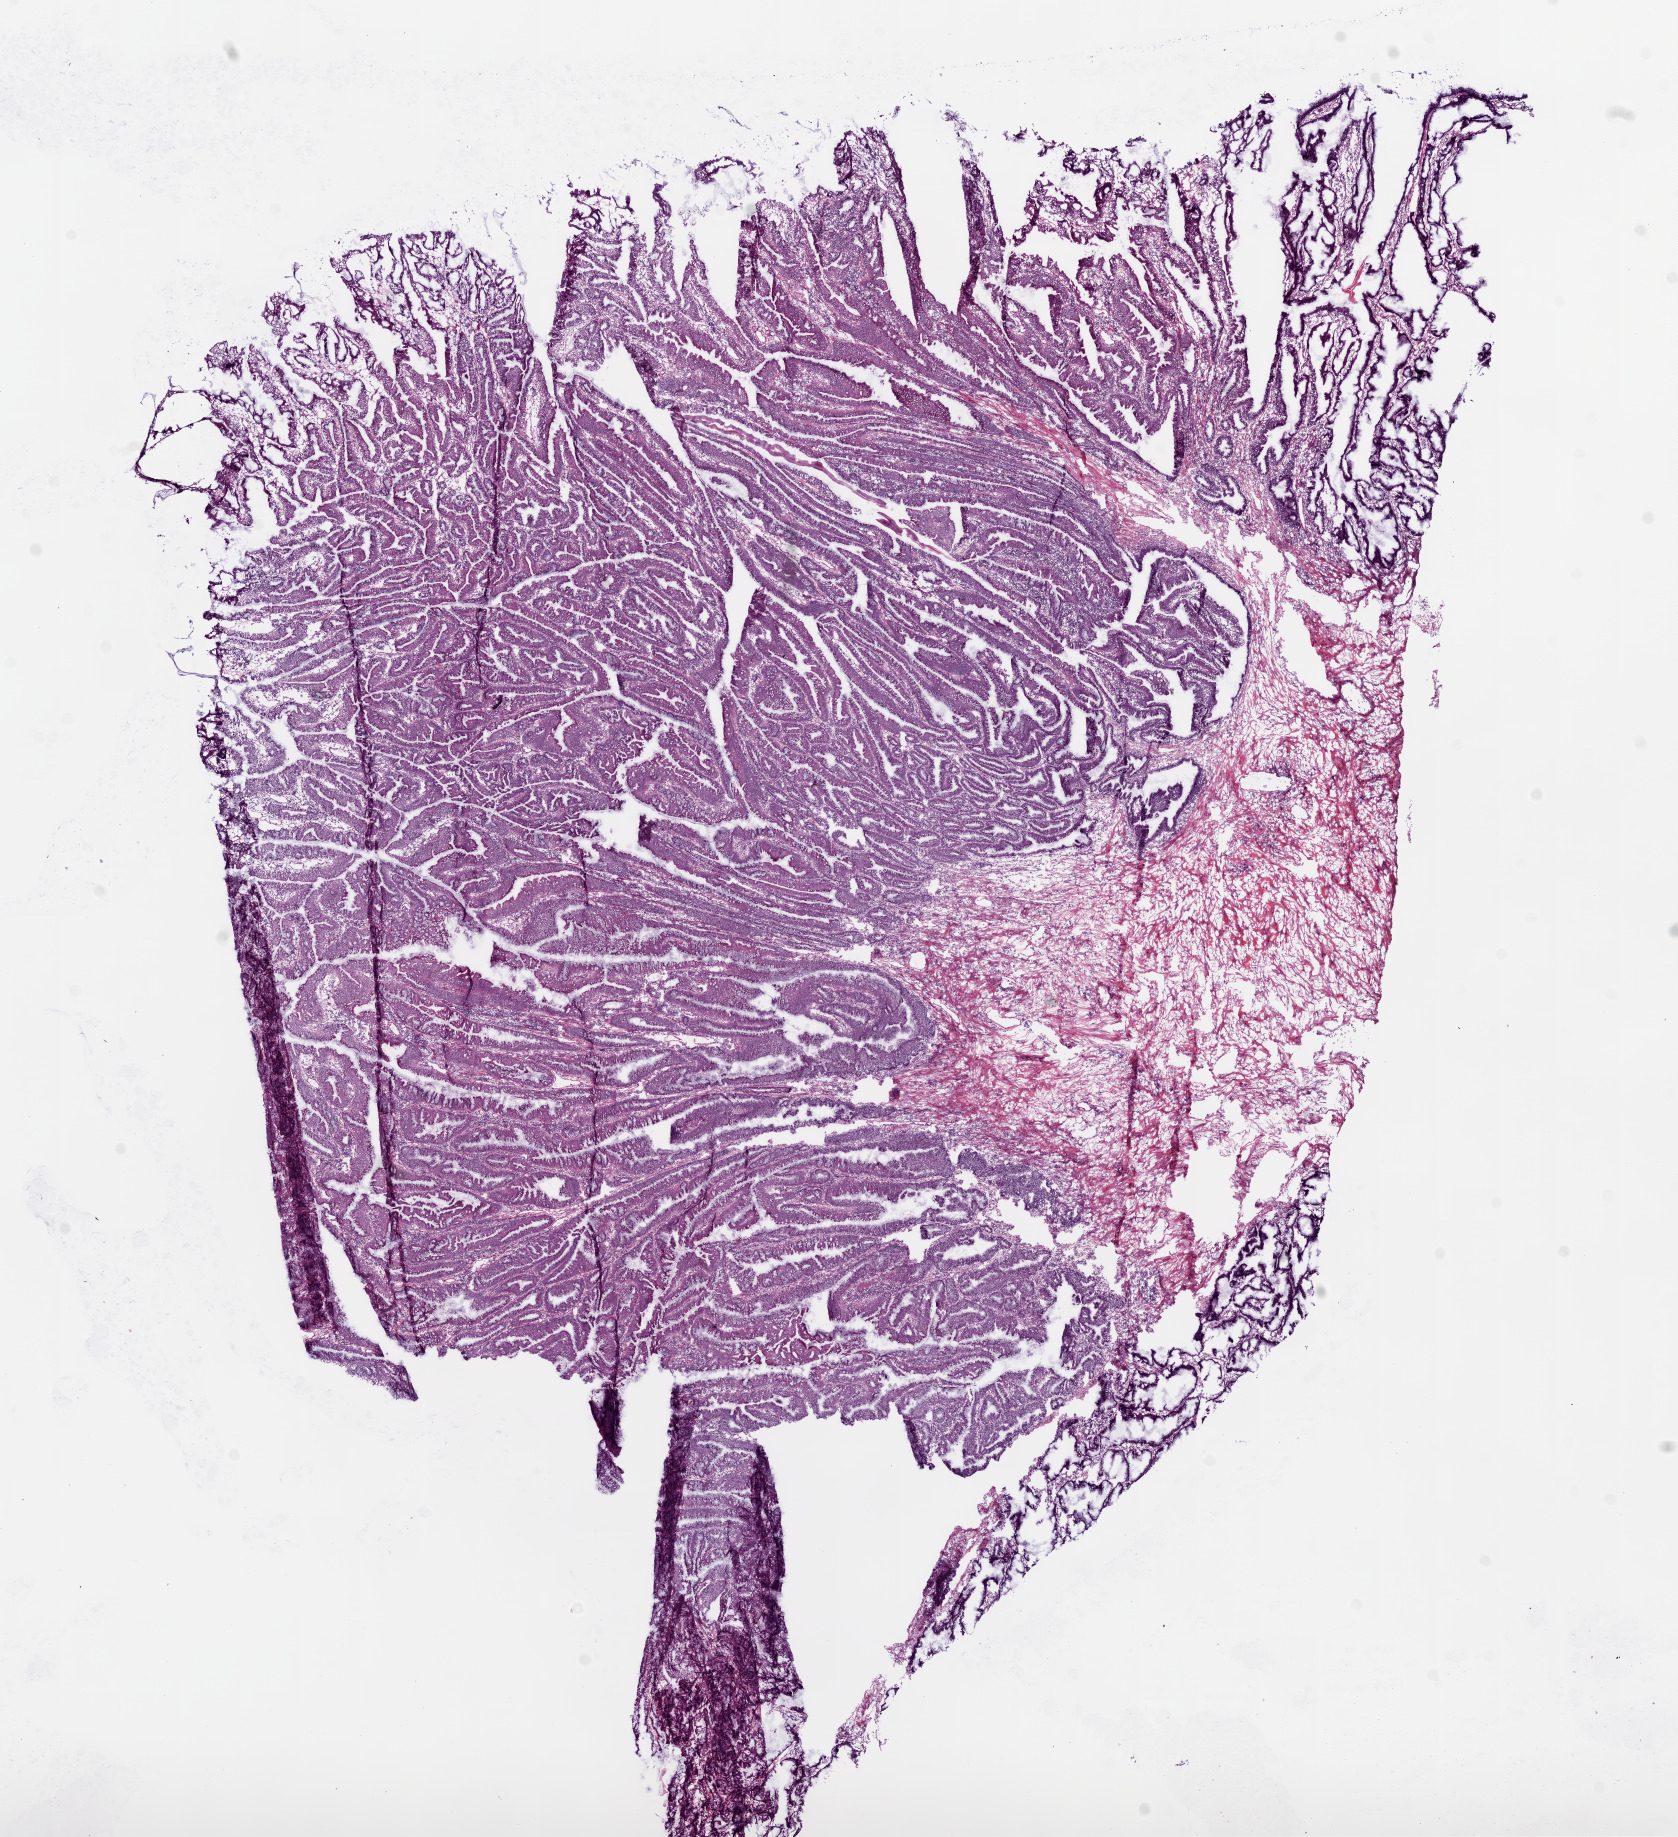
Digitized Hematoxylin and eosin (H&E) stained tissue section (whole slide), whole scanned area (about 13.5 x 14.8 mm, slide scanned at 20x) shown as a low-resolution overview, frozen section from the bottom of the tissue portion, colon, primary tumour sample. Female patient; age at initial diagnosis 52 years. Pathologist review of this section (percent, as recorded): tumour cells 85%, tumour nuclei 80%, normal cells 0%, stromal cells 15%, necrosis 0%.
• AJCC pathologic stage: IIA (6th edition)
• diagnosis: Mucinous adenocarcinoma (ascending colon)